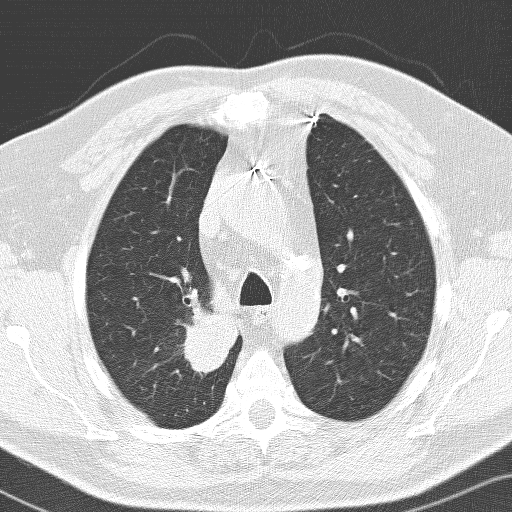
Low-dose screening chest CT, one axial slice. Slice 107 of 141 in the series (ordered by position). Lung window (W 1500 / L -600 HU). 3.2 mm slice thickness. 512 × 512 image matrix, field of view 326 × 326 mm.
Outlined on this slice (manually delineated by an expert):
- lesion 1 (tumor, upper lobe of right lung): bounding box <183,298,238,375> (left, top, right, bottom; pixels)